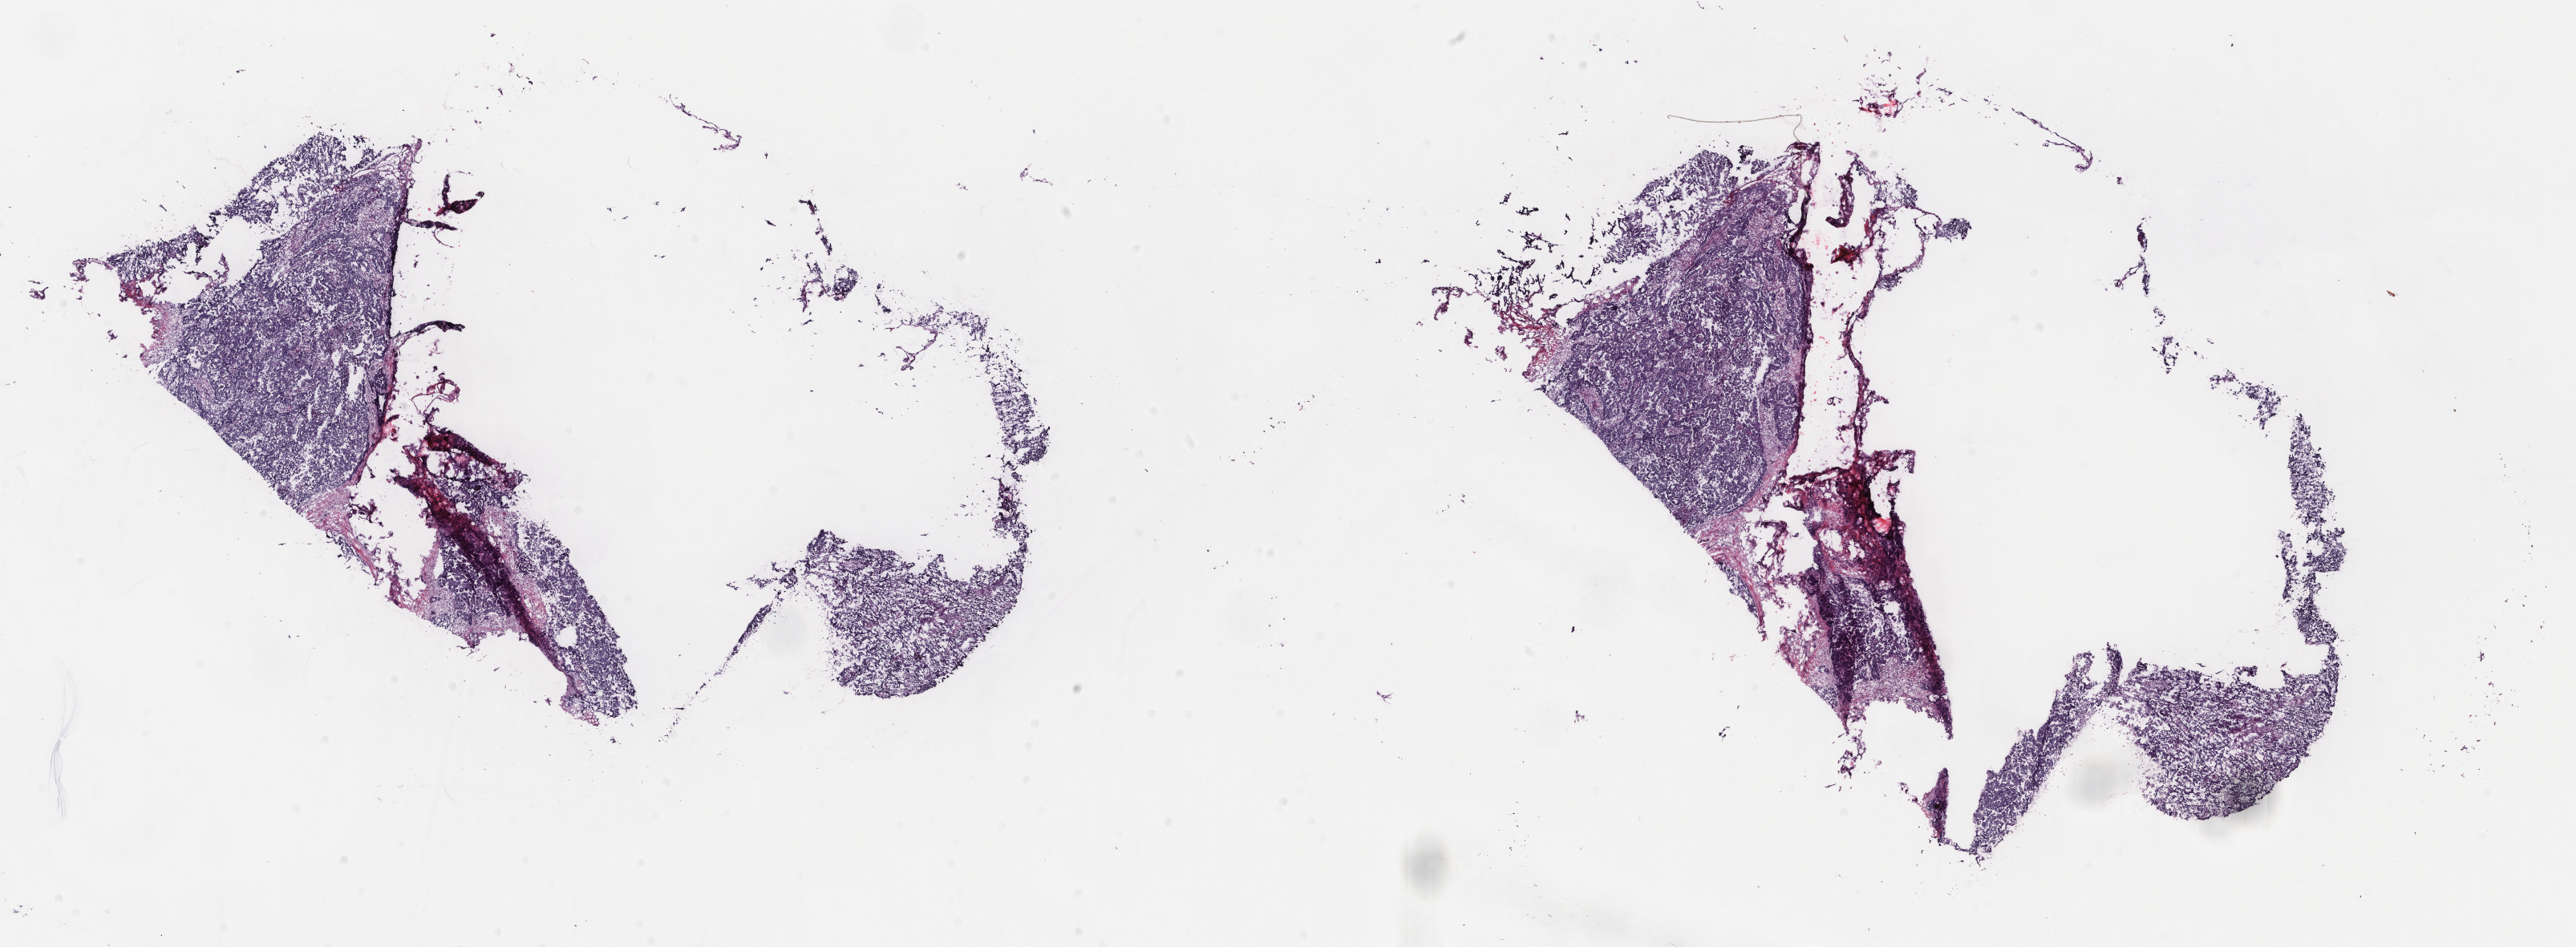
Digitized H&E tissue section (whole slide) — a low-resolution overview of the entire scanned area, about 25.5 x 9.4 mm (acquisition: 40x scan), frozen section from the top of the tissue portion, sample: primary tumour, uterus. Patient: female, age at initial diagnosis 70 years. Histologic grade: G3 (poorly differentiated). Pathologist review of this section (percent, as recorded): tumour cells 80%, tumour nuclei 88%, normal cells 10%, stromal cells 9%, necrosis 1%. Infiltration values recorded for this section: lymphocyte infiltration 4%, monocyte infiltration 0%, neutrophil infiltration 1%.
- histologic diagnosis: Serous cystadenocarcinoma, NOS (endometrium)
- FIGO stage: IIB
- lymph nodes positive (case pathology): 0 of 17 examined